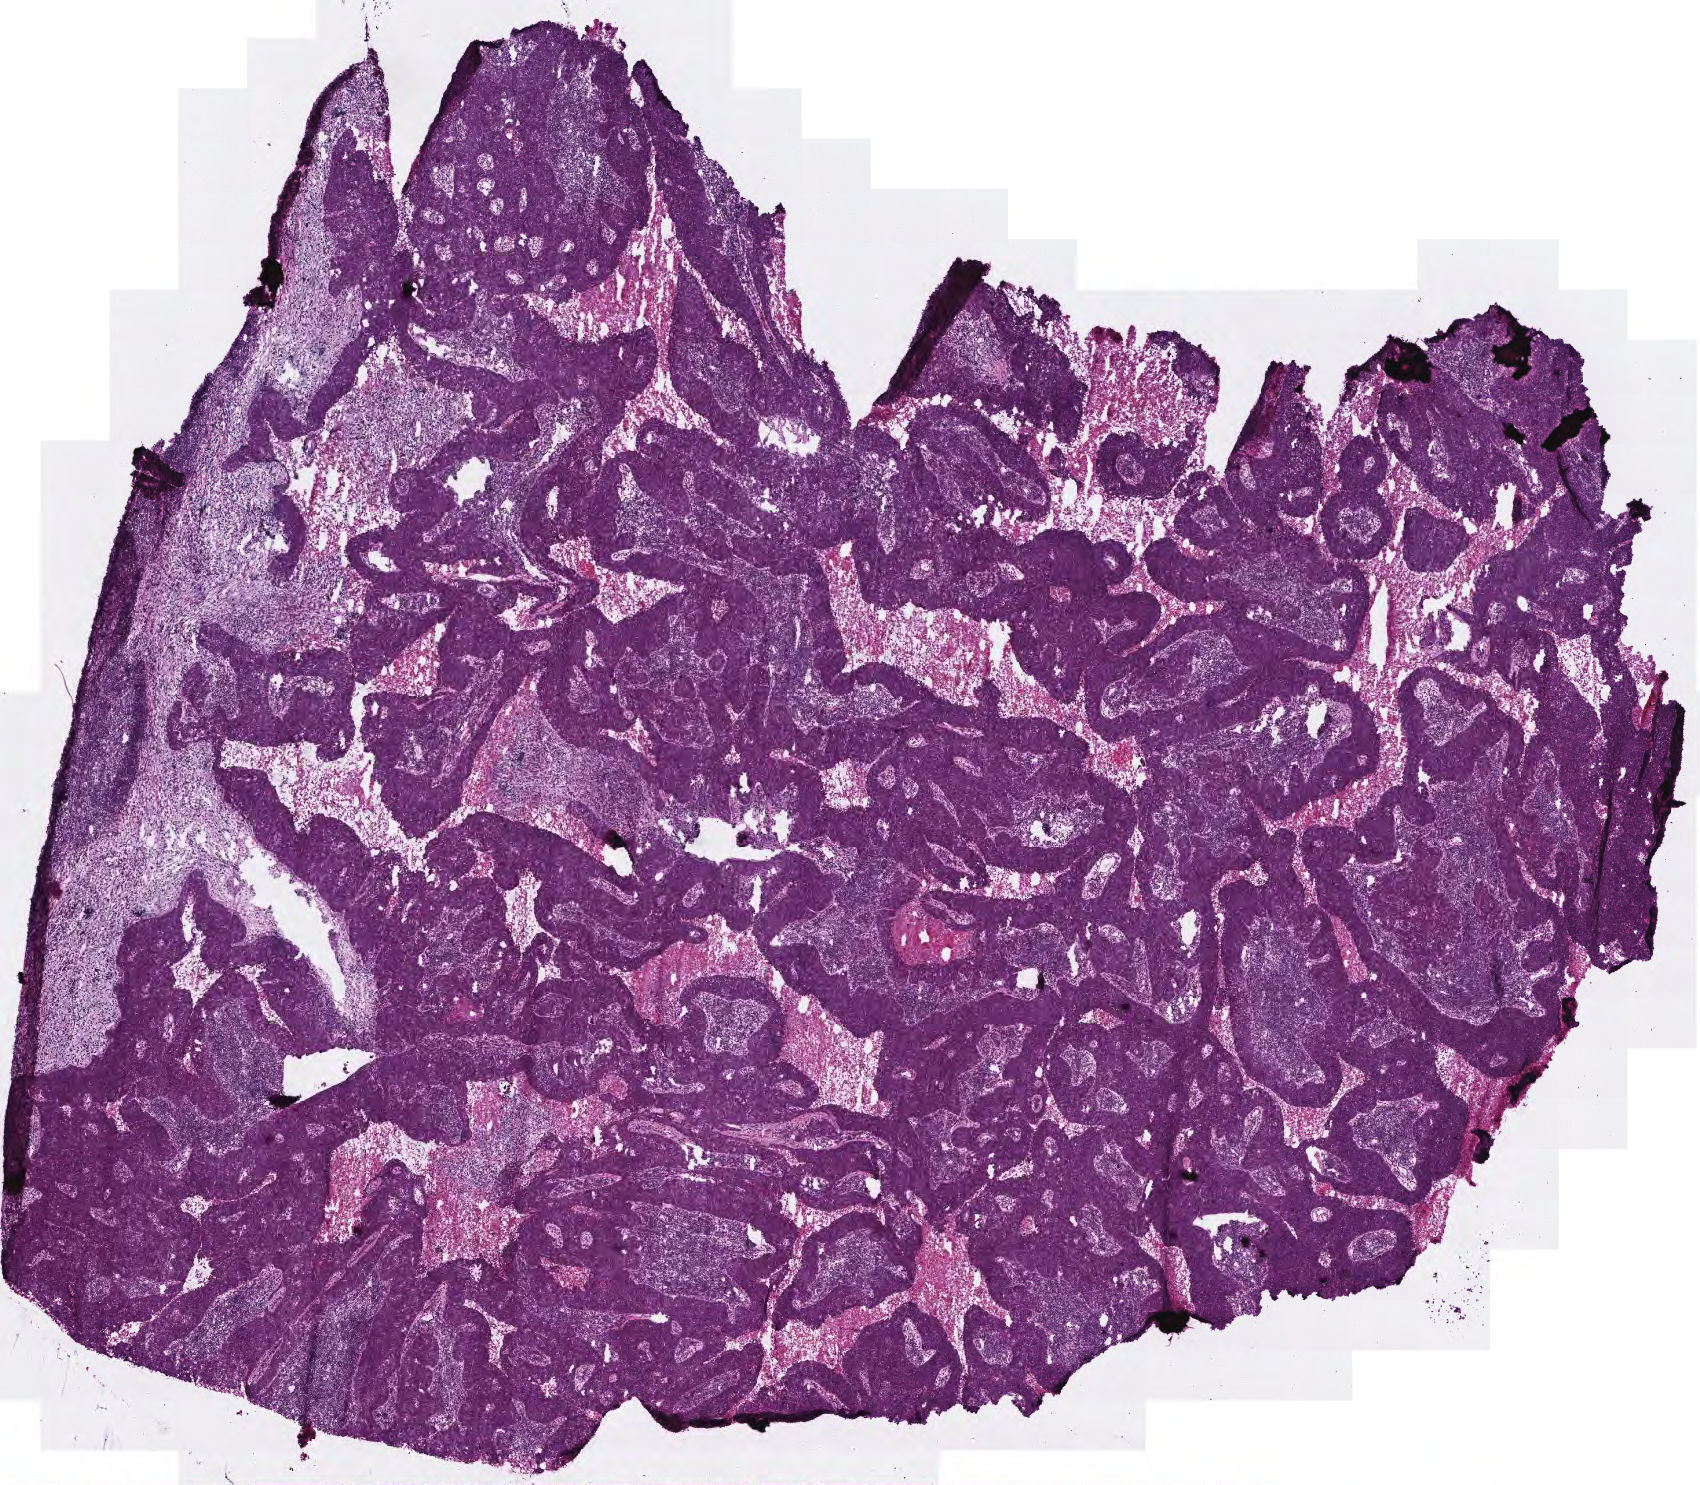
H&E-stained whole-slide image, low-resolution overview of the scanned area, about 3.4 x 3.0 mm. Frozen section from the top of the tissue portion. Primary tumour sample from the head and neck. Male patient; age at initial diagnosis 59 years. Histologic grade: G3 (poorly differentiated). Slide review estimates, as recorded: tumour cells 75%, tumour nuclei 80%, normal cells 0%, stromal cells 15%, necrosis 0%.
• histologic diagnosis: Squamous cell carcinoma, NOS (tonsil, NOS)
• AJCC pathologic stage: III (6th edition)
• TNM: T2 N1 M0
• laterality: right